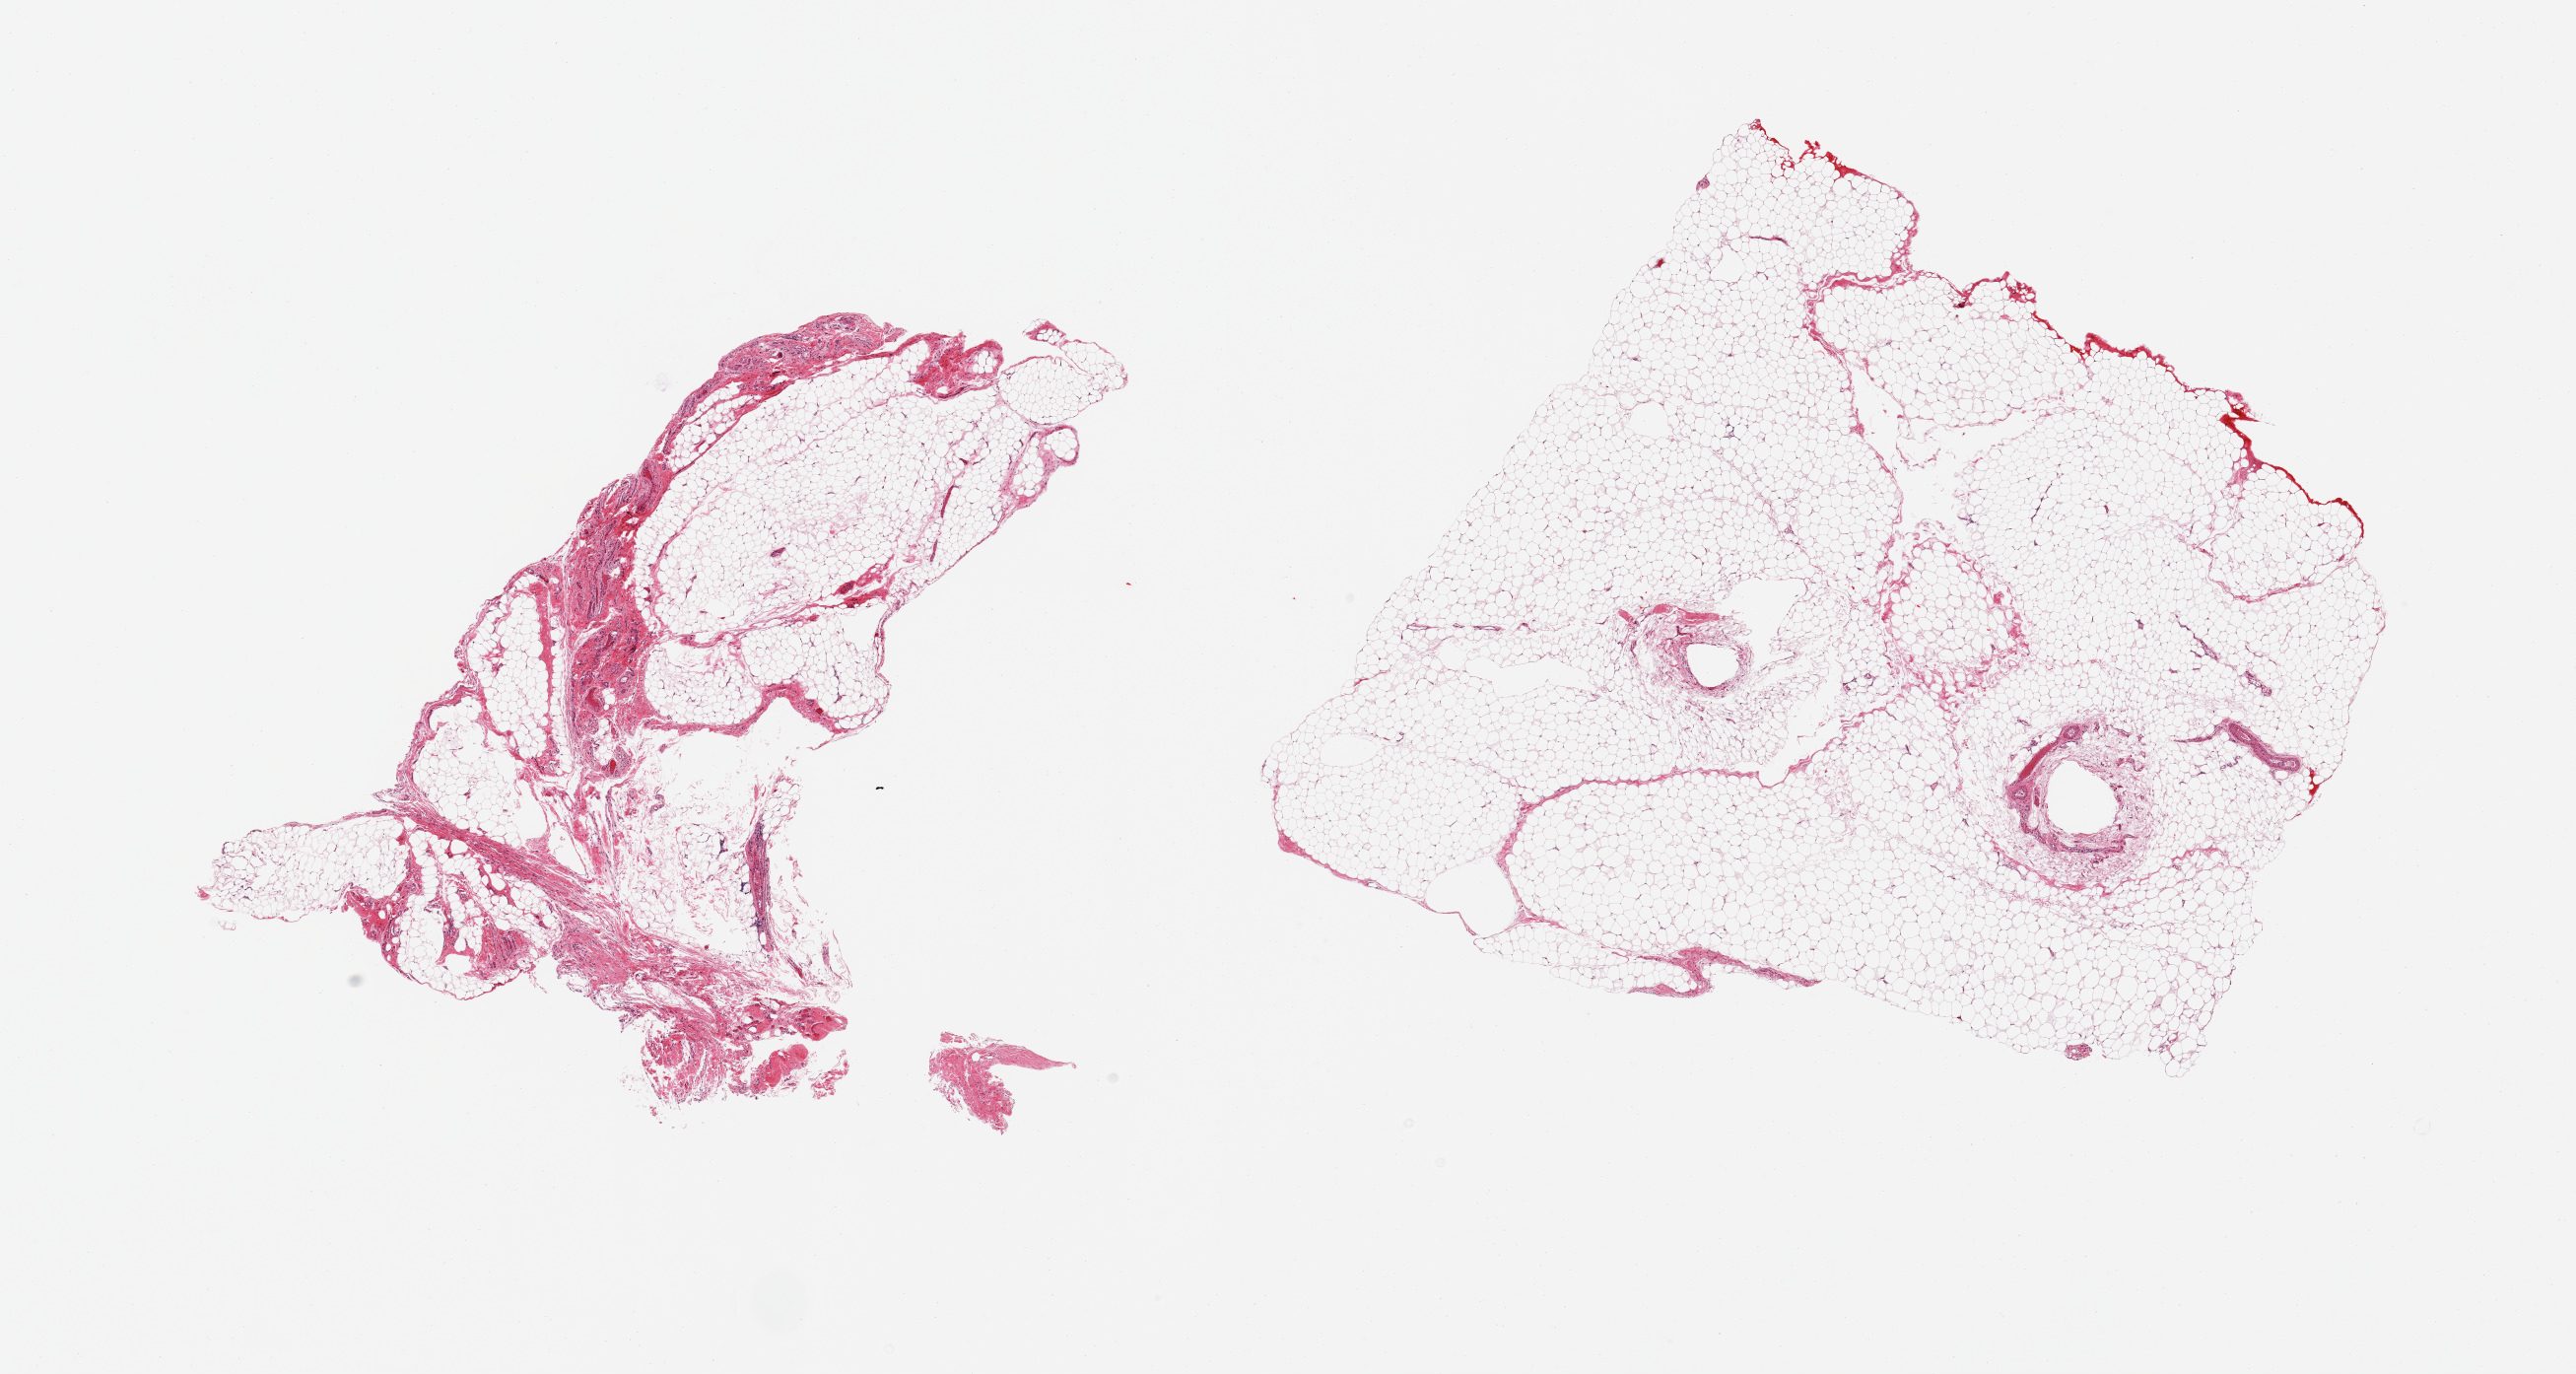
Whole-slide image, hematoxylin and eosin (H&E) stain — low-resolution overview of the scanned area, about 20.7 x 11.0 mm, PAXgene-fixed, paraffin-embedded tissue, sampled site (target tissue): omentum, donor tissue sample. Donor: male.
• pathologist's review note for this sample: 2 pieces, ~20% fascia